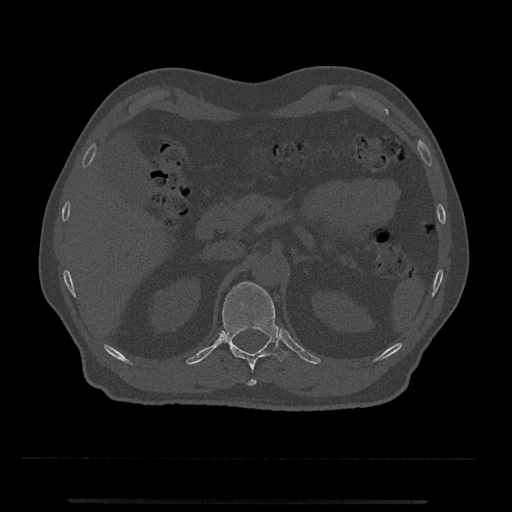
CT including the spine, one axial slice. Slice 399 of 797 in the series (ordered by position). Bone window (W 1800 / L 400 HU). 0.5 mm slice thickness. 512 × 512 image matrix, field of view 419 × 419 mm. Patient: male, 63 years. From the clinical record (not read from this slice): primary cancer: prostate.
Structures marked on this image (semi-automatic segmentation, software-assisted and operator-edited):
- T12 vertebra: bounding box [x1, y1, x2, y2] px = [221, 282, 289, 386]